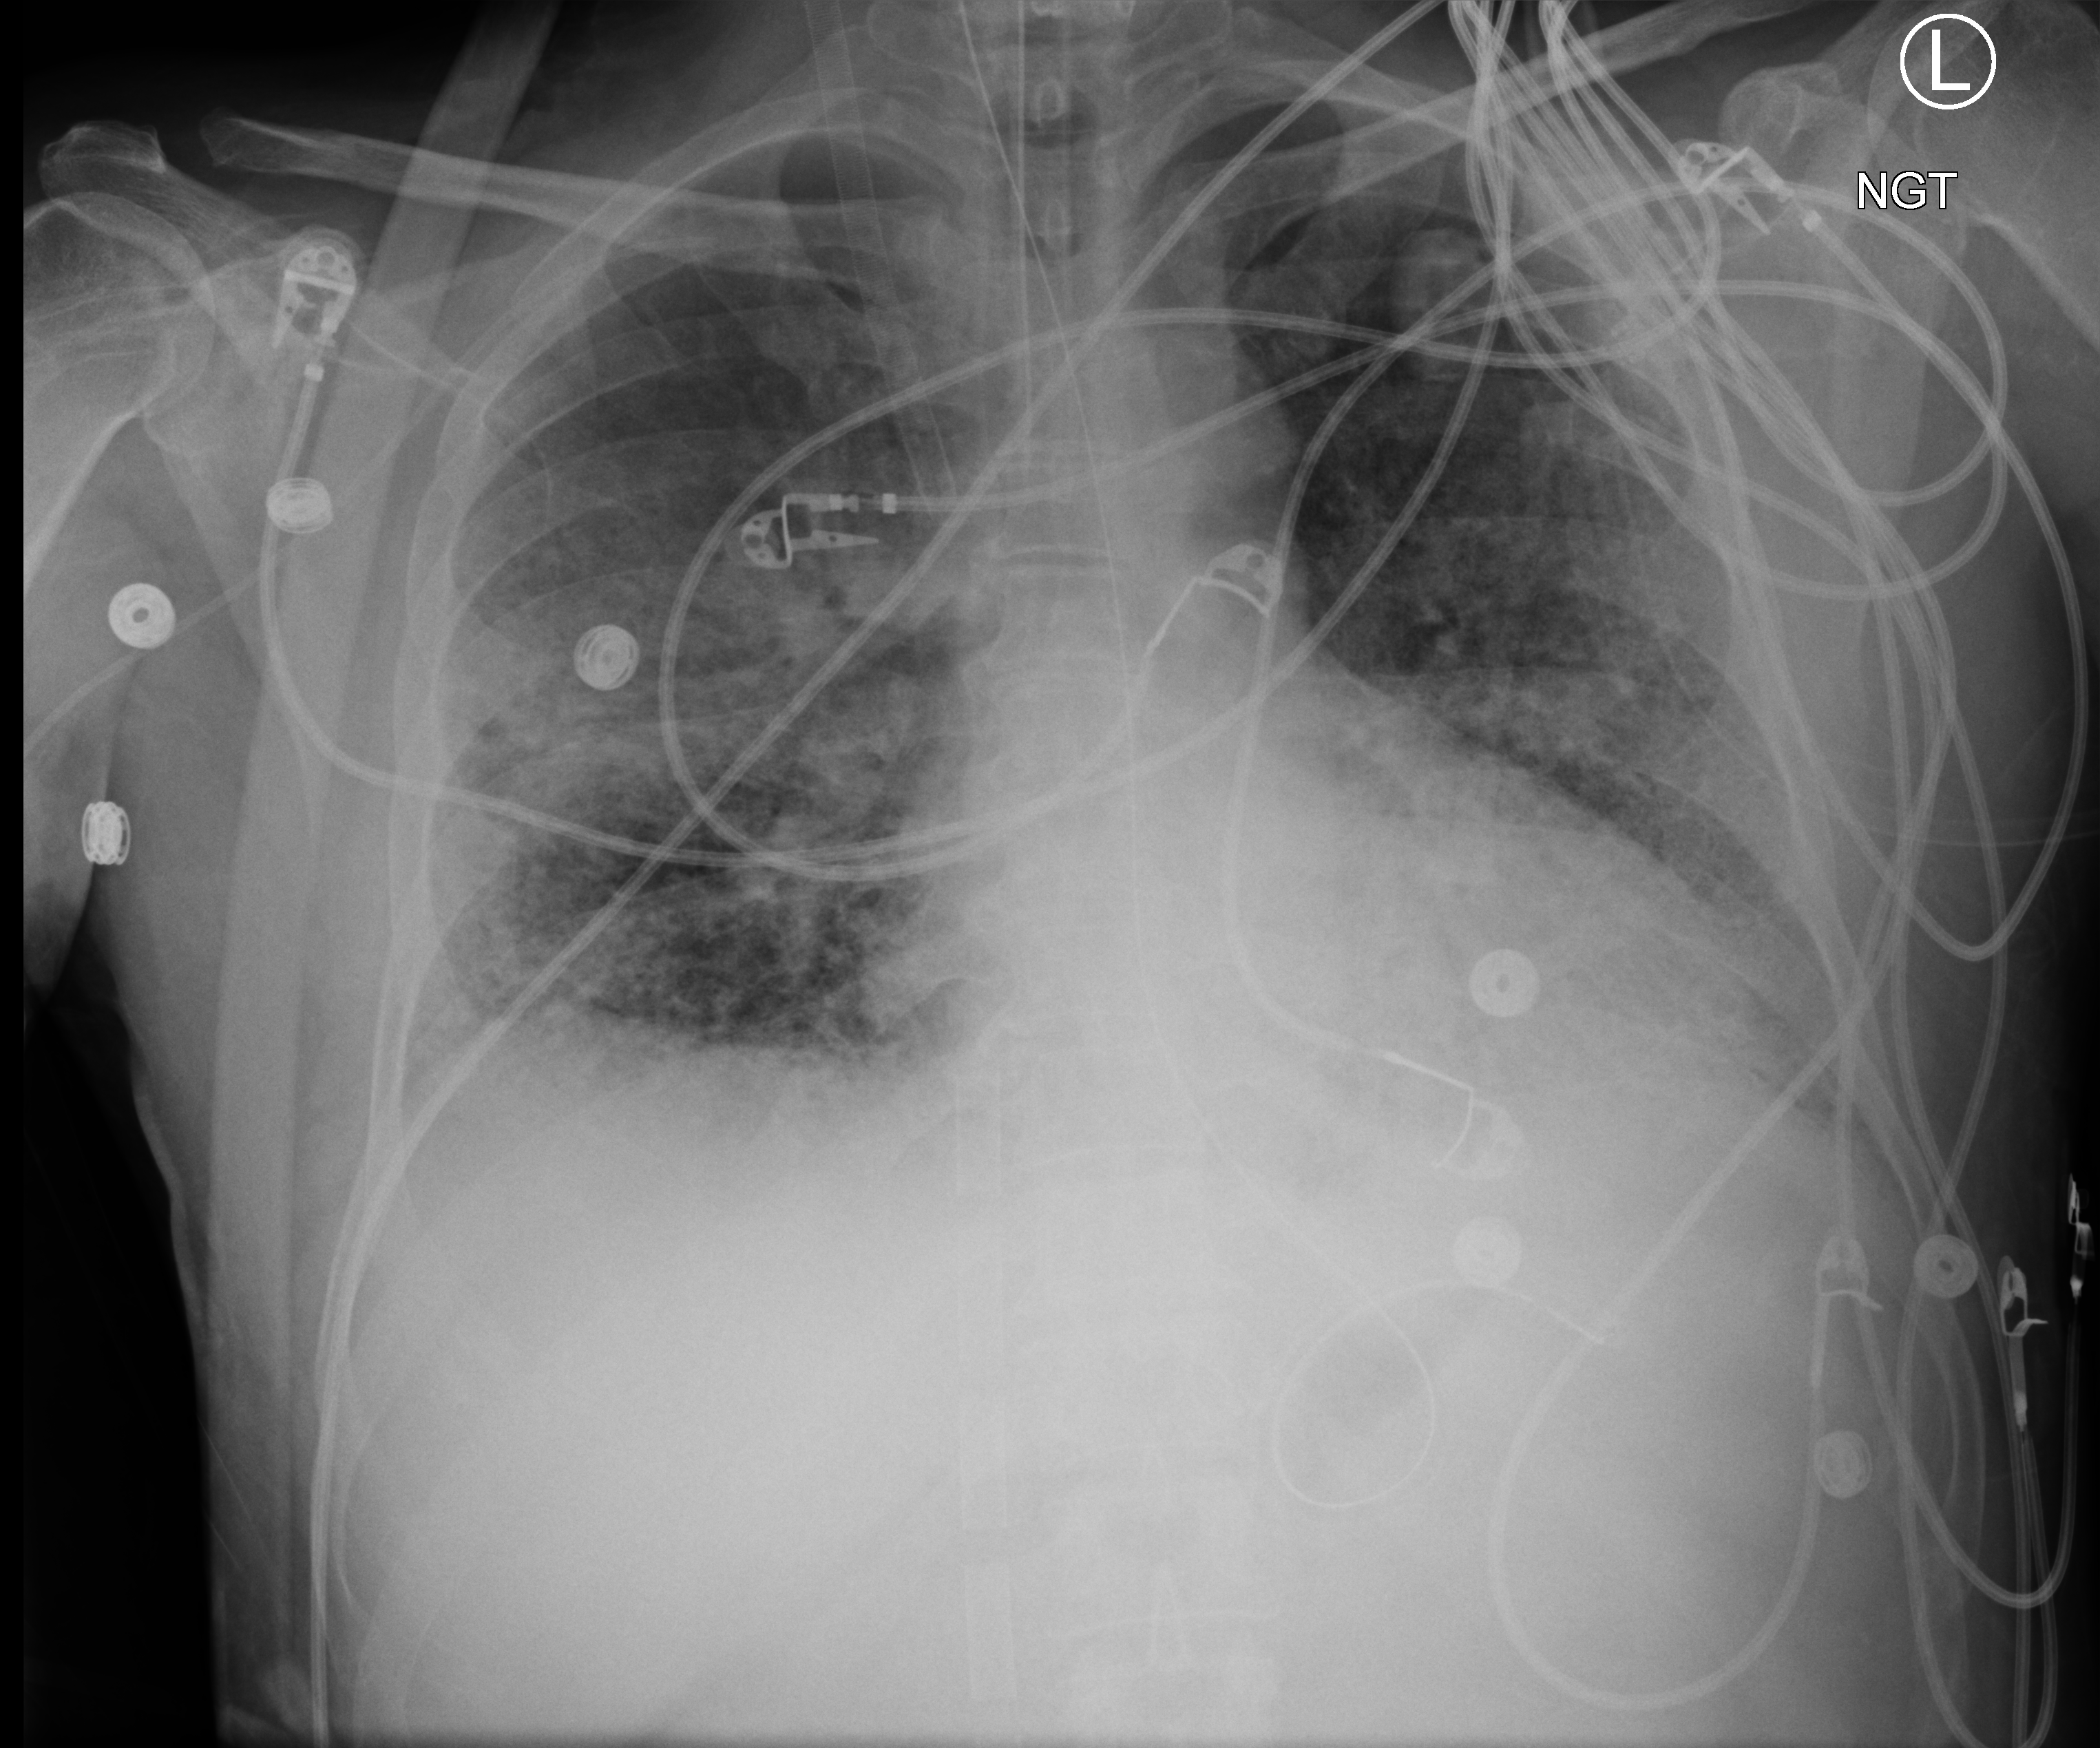
Portable chest radiograph, anteroposterior (AP) projection. Male patient hospitalised with COVID-19, age 18–59 years.
Admission-level facts for this patient (not findings on this image; timing relative to this image not recorded): mechanically ventilated during this hospital stay: yes; admitted to intensive care during this hospital stay: yes.